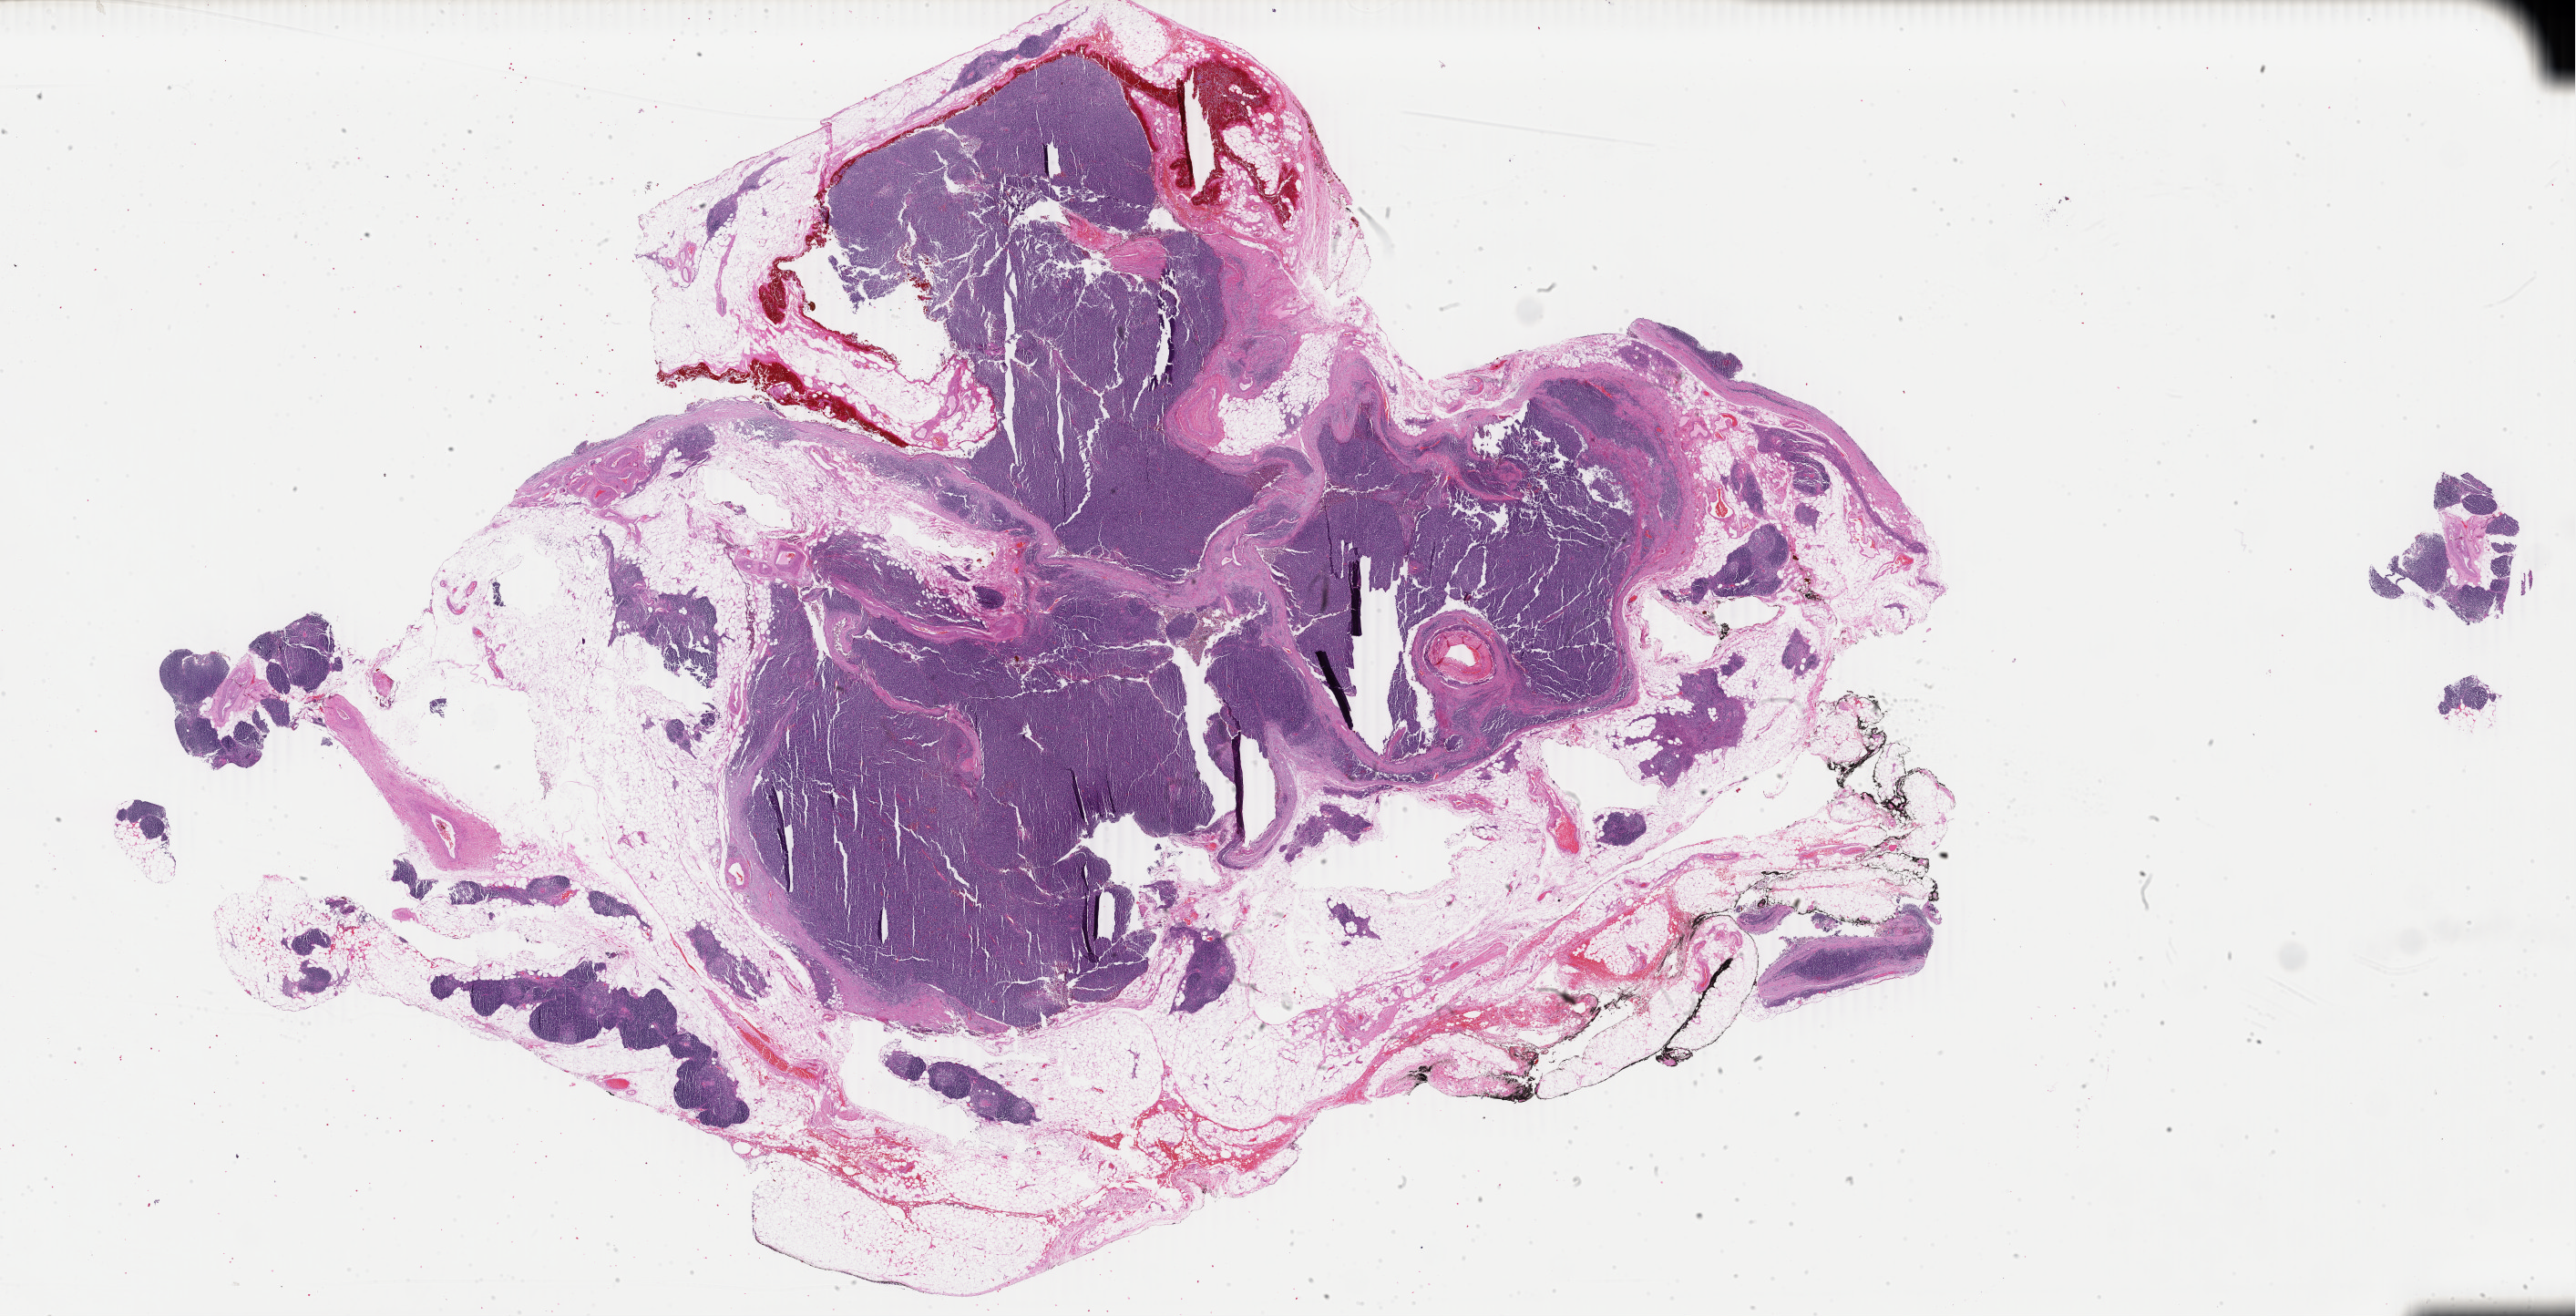
Whole-slide histology image, H&E — whole scanned area (about 45.0 x 23.0 mm, acquisition: 40x scan) shown as a low-resolution overview. FFPE section. Primary tumour sample from the thymus. Patient: male, age at initial diagnosis 71 years.
* diagnosis: Thymoma, type B2, malignant